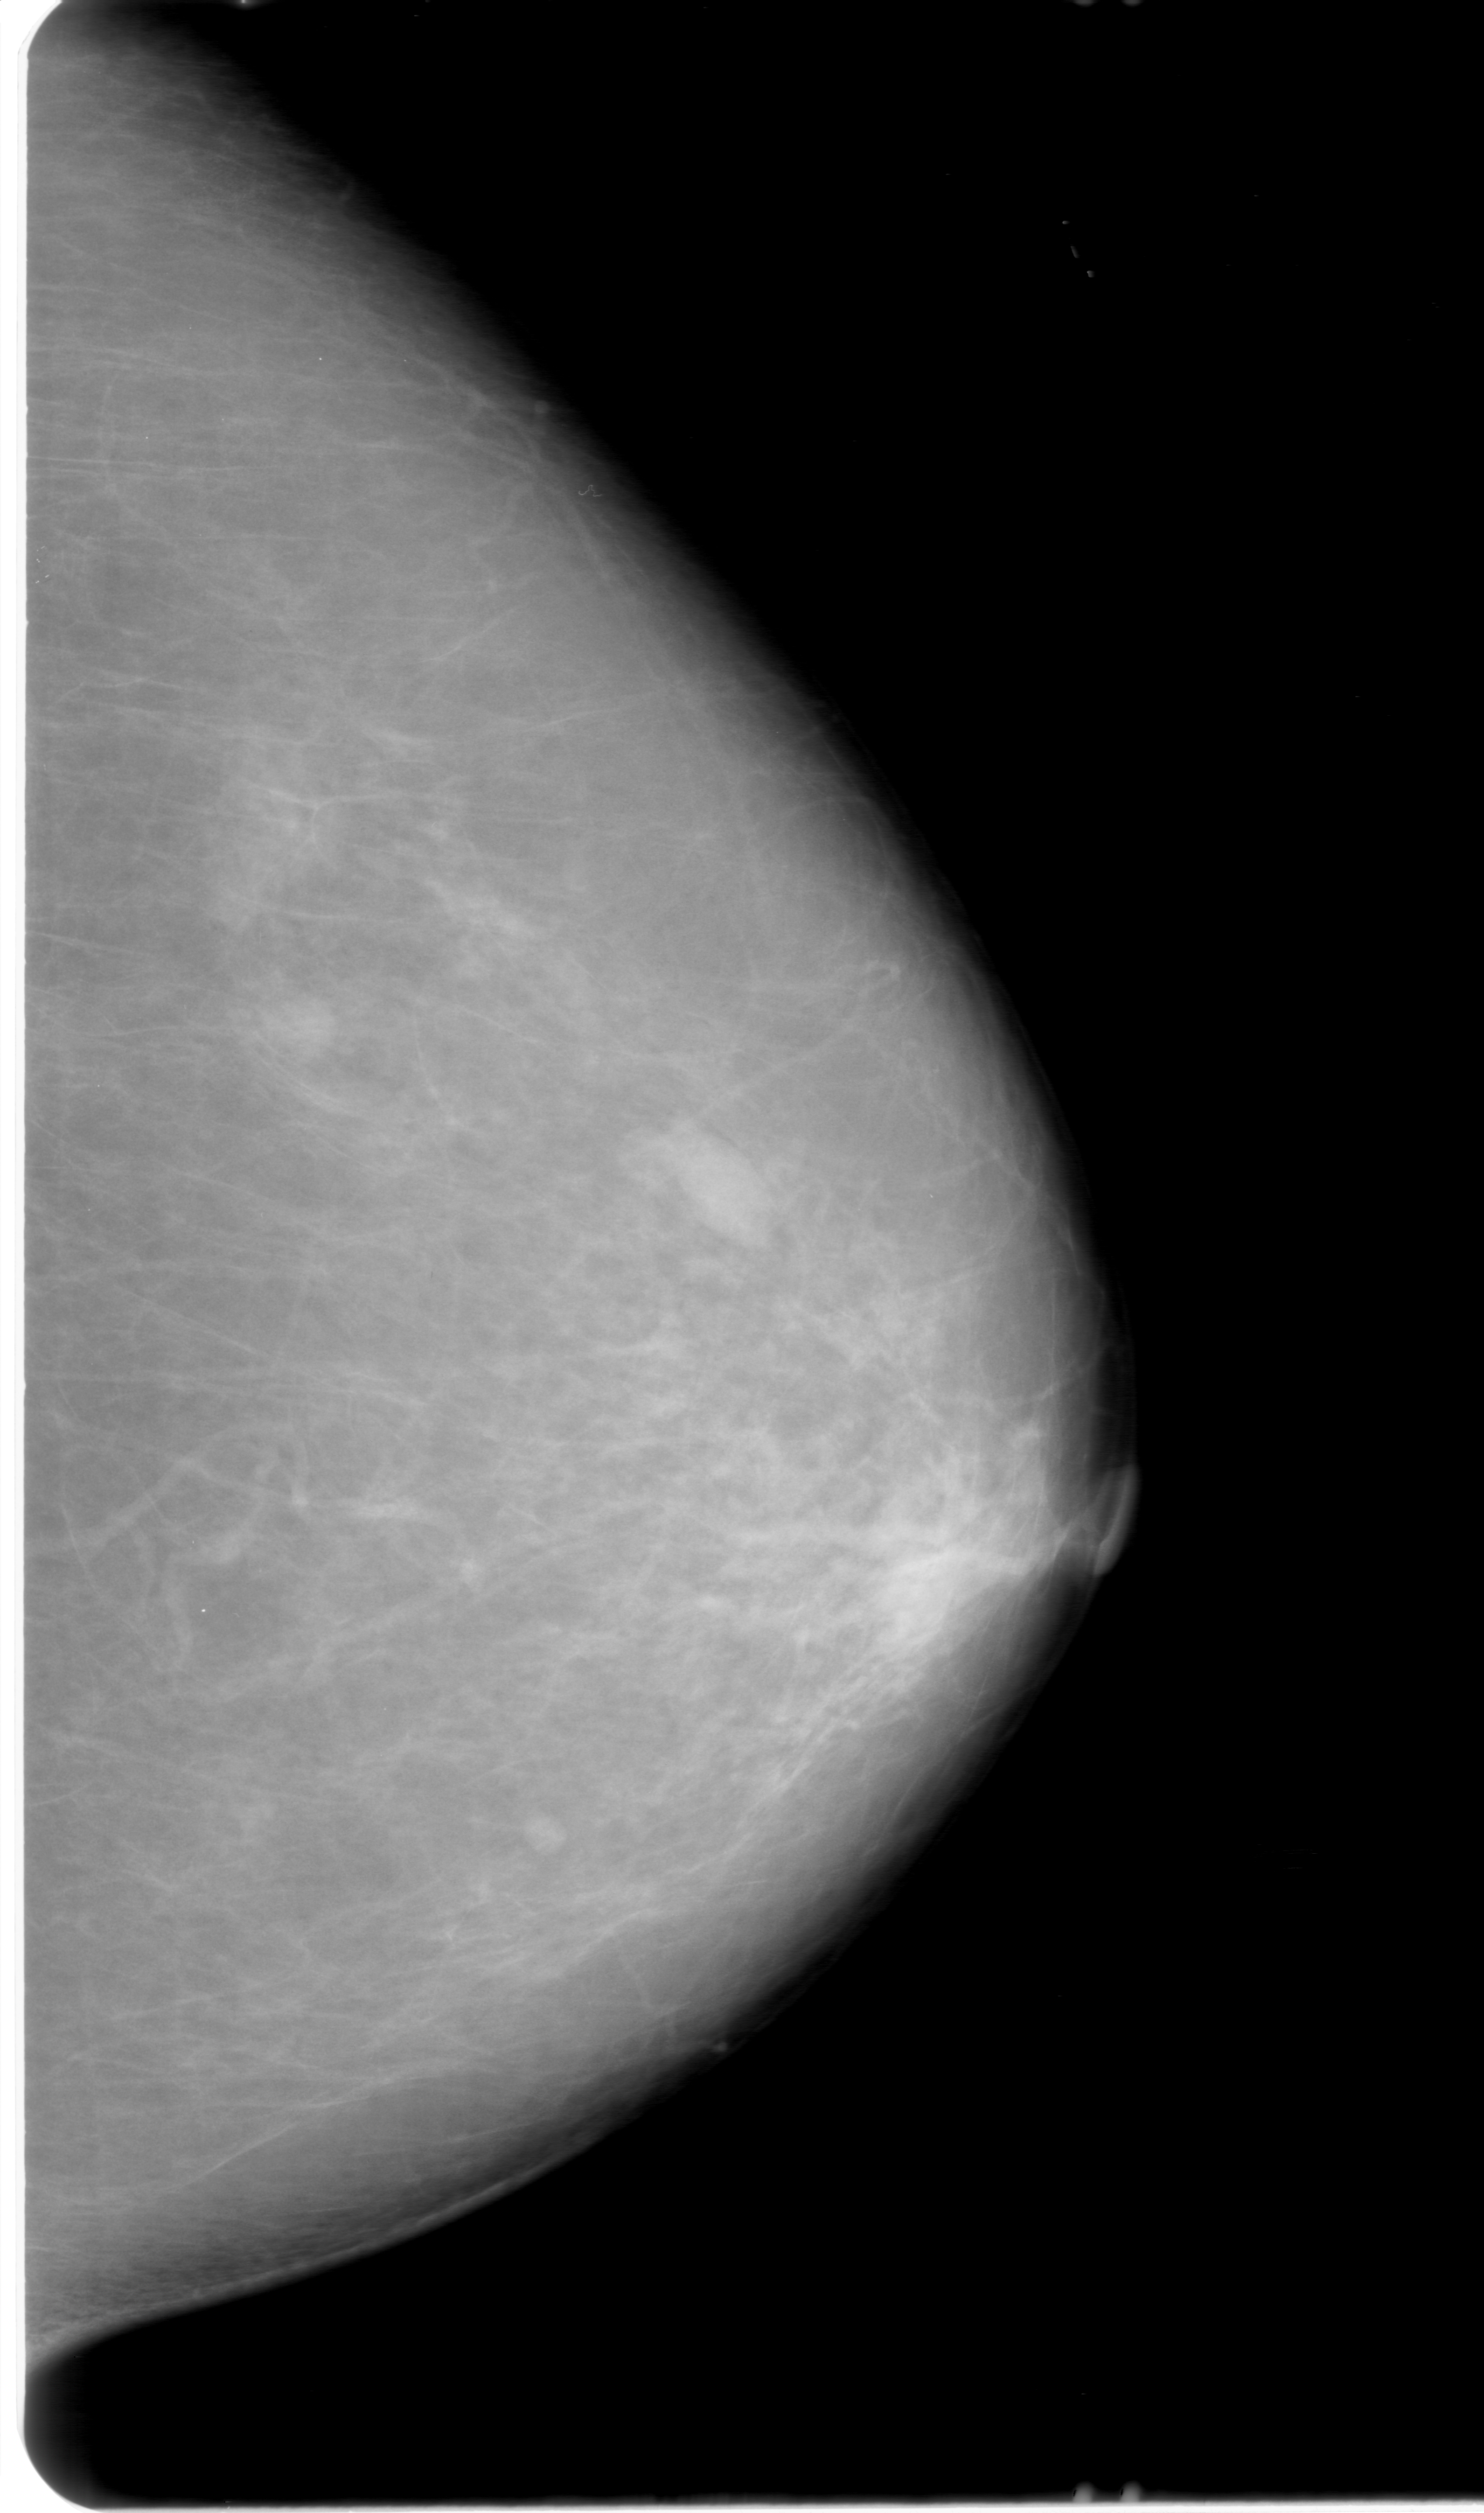
Digitized screen-film mammogram. Left breast. Craniocaudal (CC) view. 1484 × 2513 image matrix.
Expert-marked regions of interest on this film, with their recorded descriptors:
- mass, shape oval, margins obscured; BI-RADS assessment category 0 (incomplete: needs additional imaging); subtlety rating 5 on a 1 (subtle) to 5 (obvious) scale; pathology result (as recorded, not read from the image): benign: bounding box <678,1139,773,1236> (left, top, right, bottom; pixels)